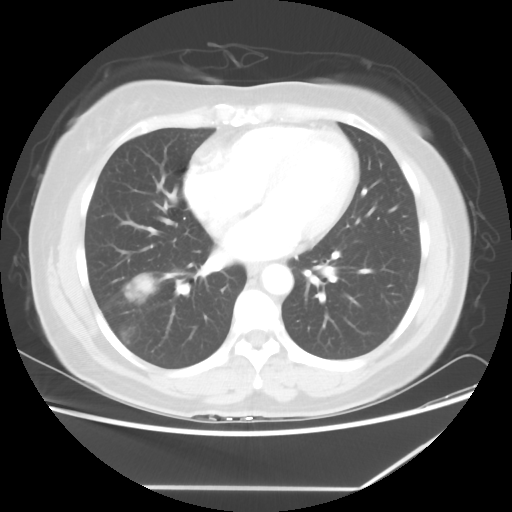
Chest CT, one axial slice; position 26 of 60 along the scan axis; lung window (W 1500 / L -600 HU); 5 mm slice thickness; 512 × 512 image matrix. Female patient, age 42 years. Case-level facts recorded for this patient, not image findings: clinical TNM (as recorded): T2 N1 M0.
Annotated regions visible in this slice (bounding box drawn by a radiologist):
- lung tumour (recorded histology: adenocarcinoma): bounding box <132,271,155,299> (left, top, right, bottom; pixels)